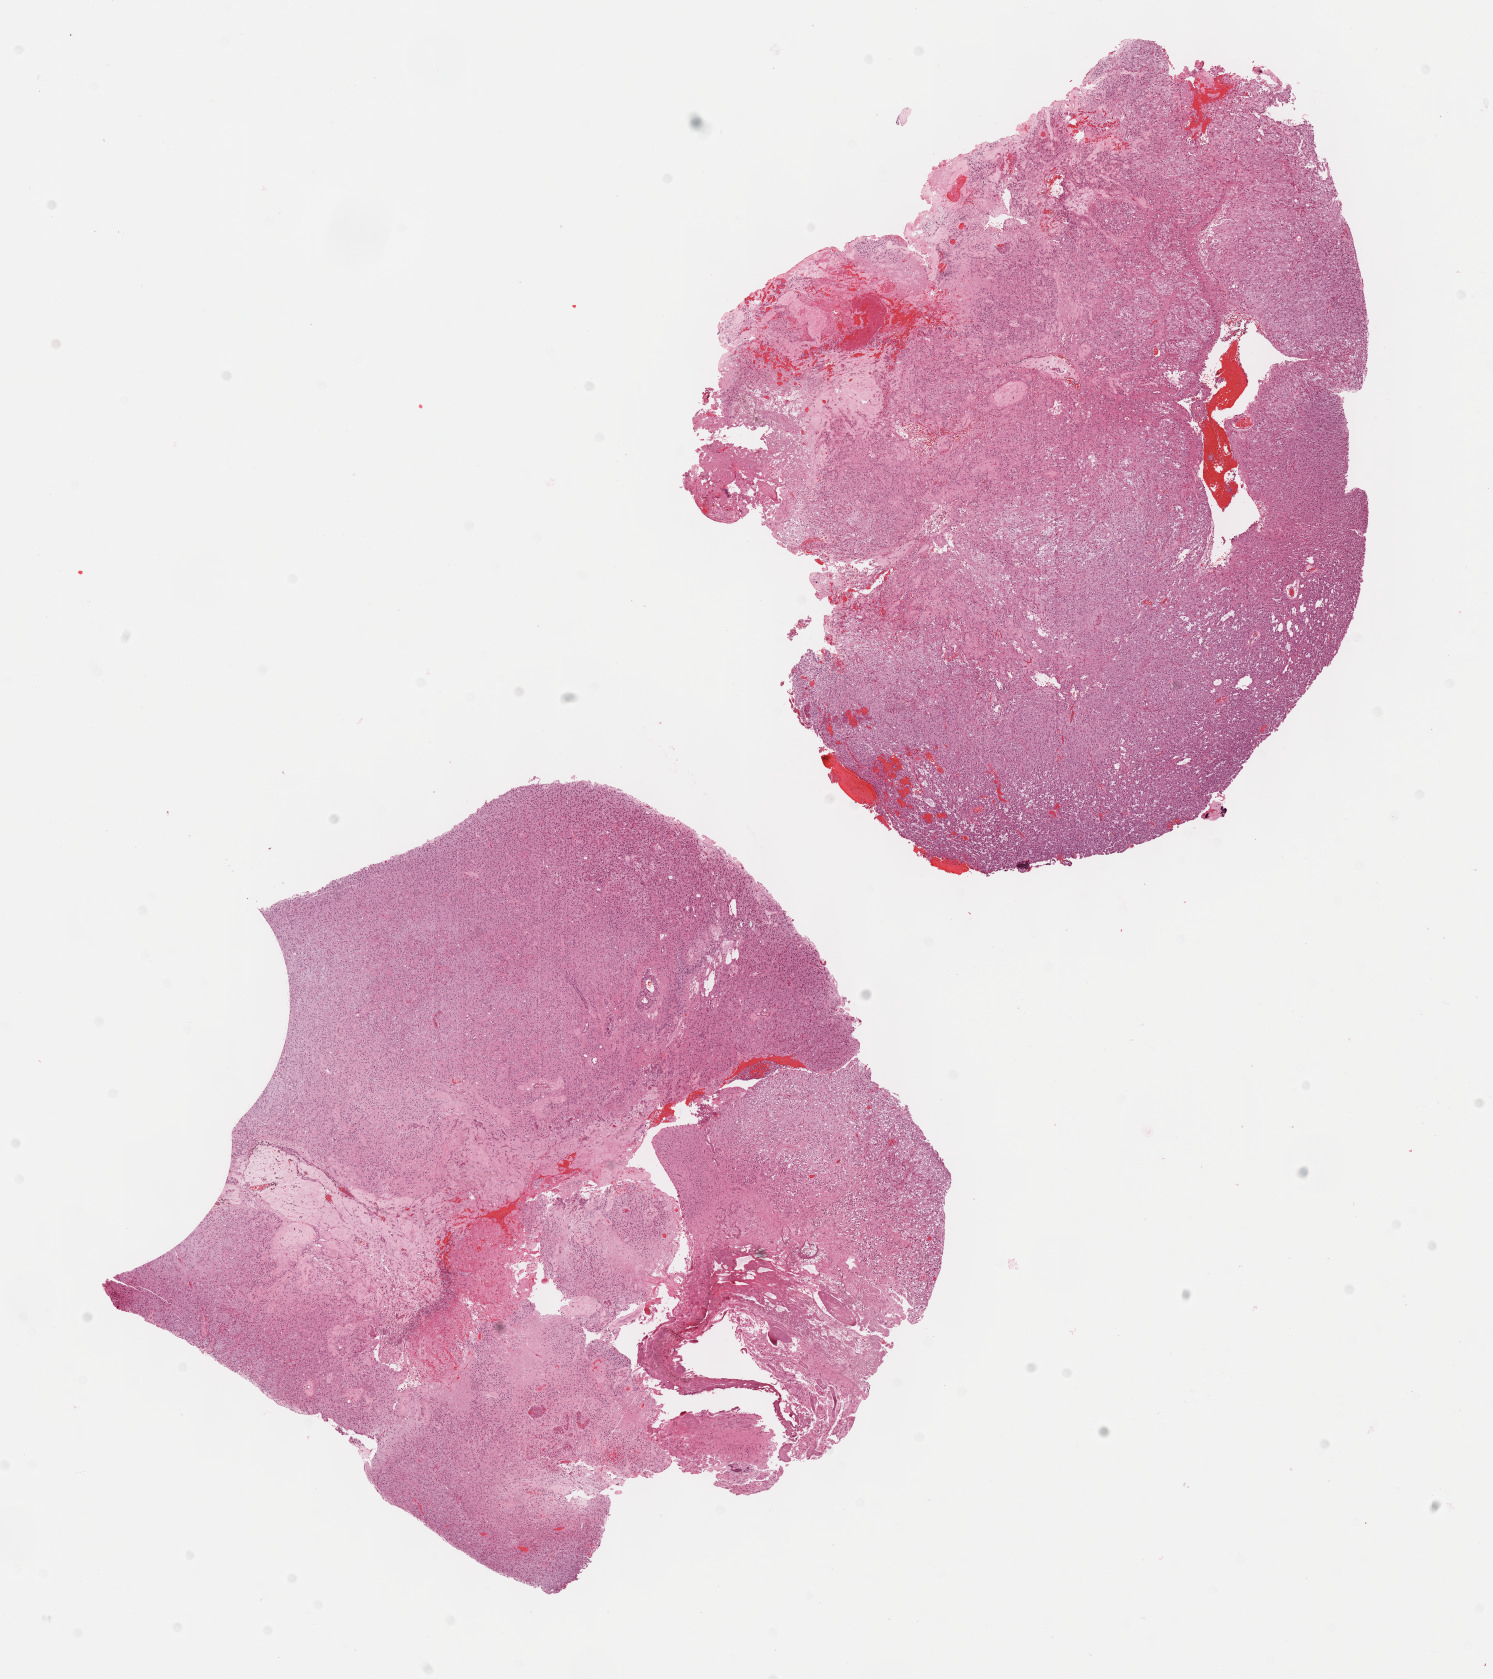
Whole-slide histology image, Hematoxylin and eosin (H&E) stained — a low-resolution overview of the entire scanned area, about 12.1 x 13.6 mm. FFPE section. Brain, primary tumour sample. Male, age 47 years at initial diagnosis. Histologic grade: G3 (poorly differentiated).
* laterality: left
* histologic diagnosis: Oligodendroglioma, anaplastic (cerebrum)